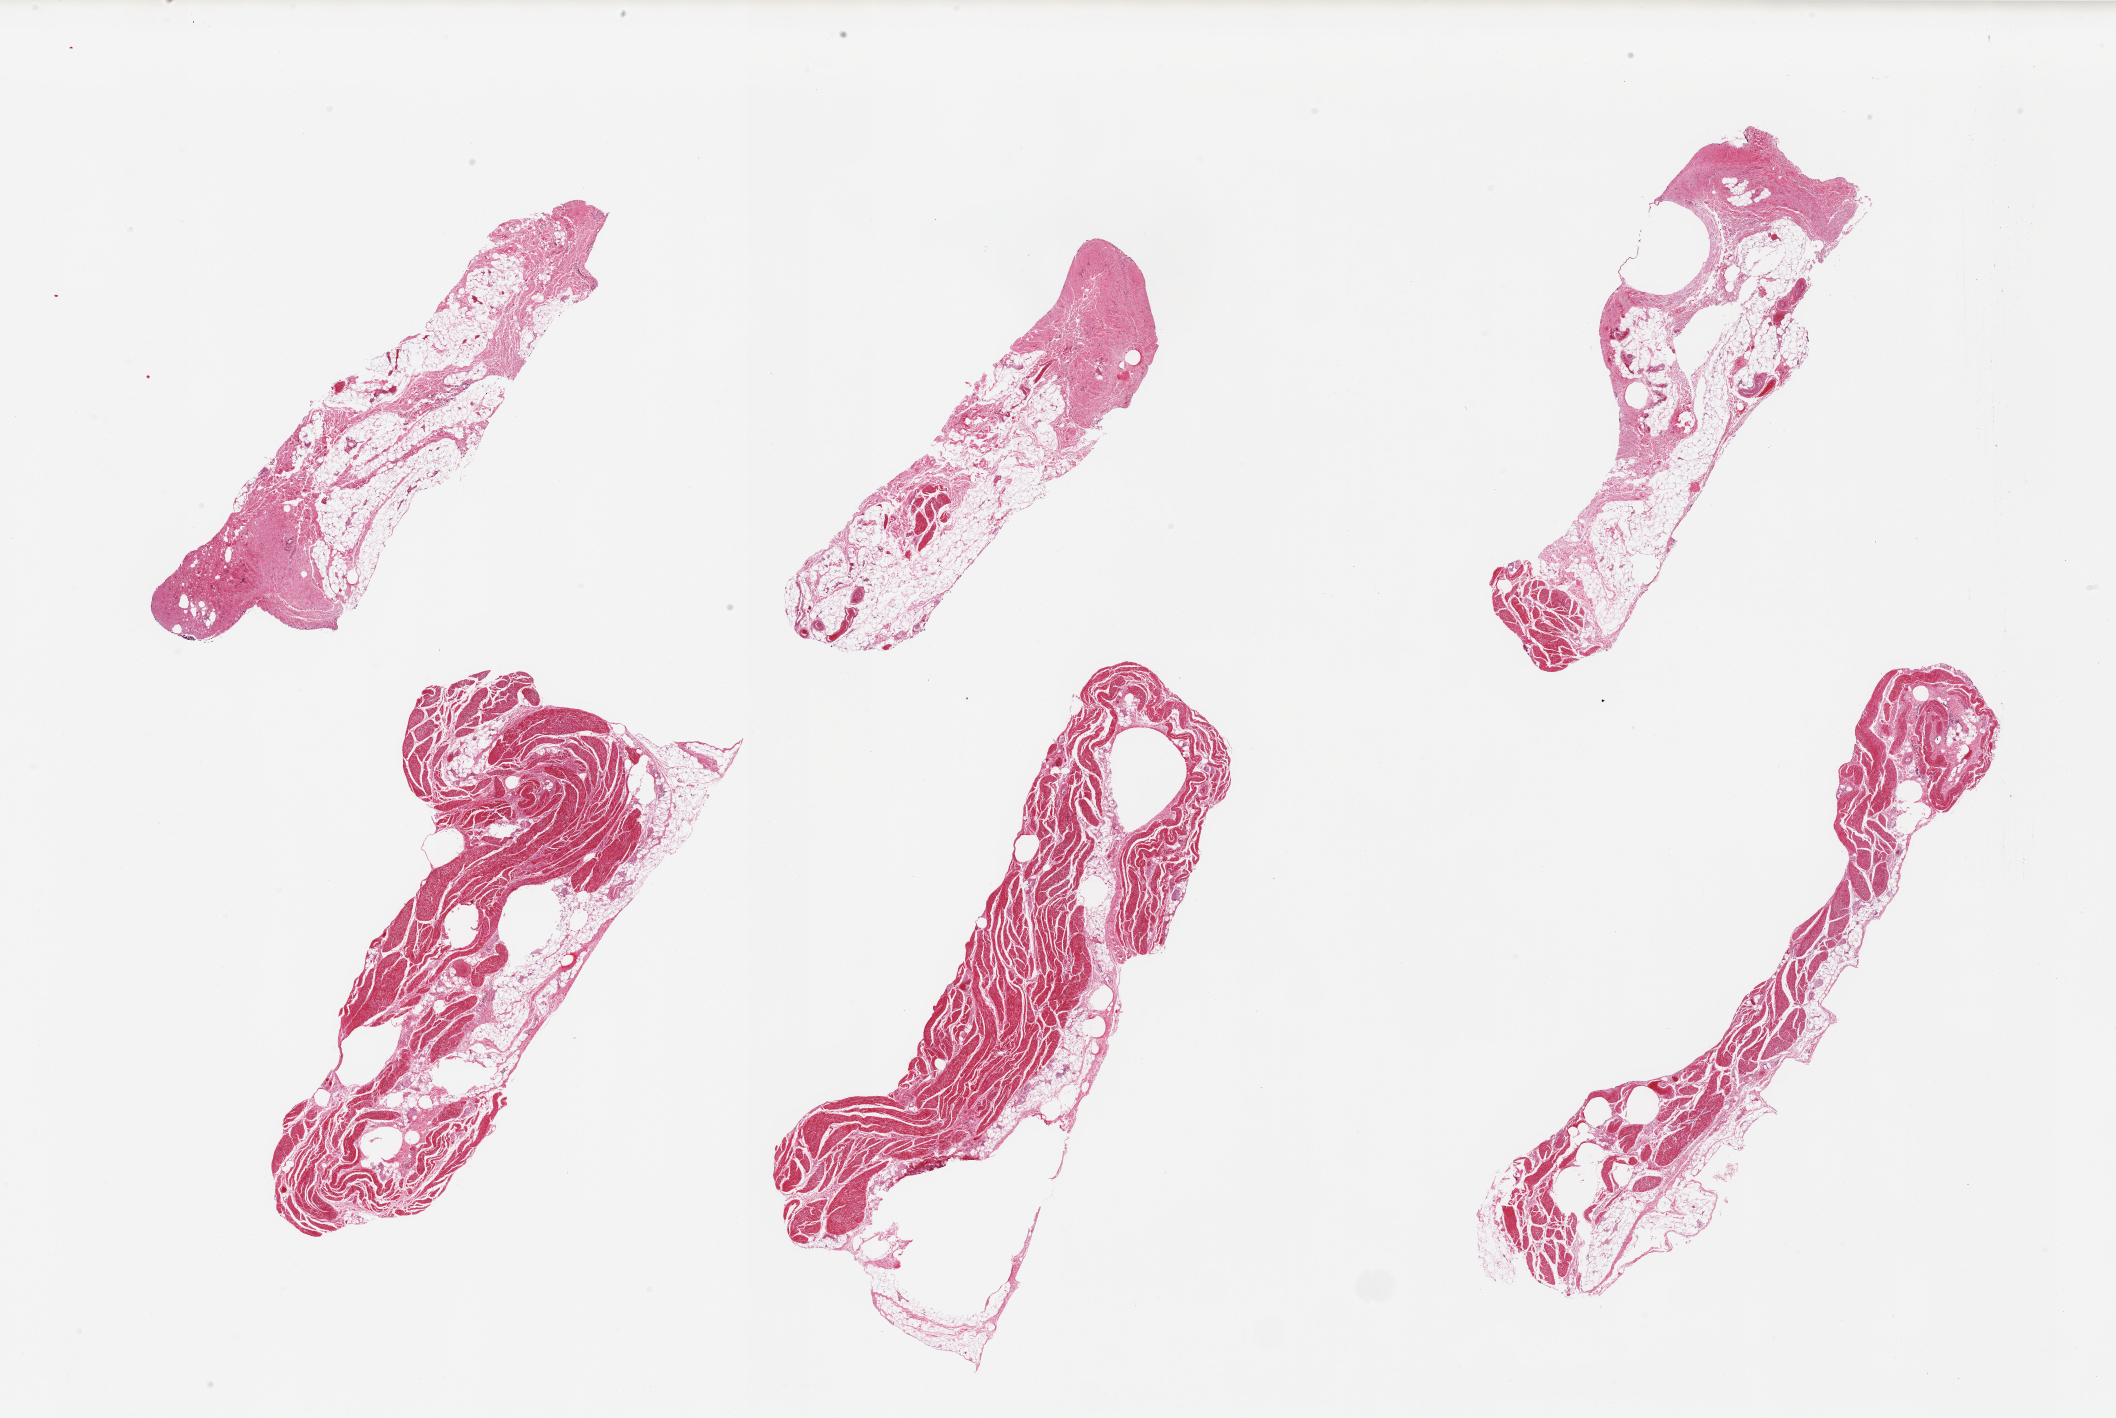
Haematoxylin and eosin whole-slide image, brightfield — shown as a low-resolution overview of the whole scanned area (about 33.5 x 22.4 mm); PAXgene-fixed, paraffin-embedded tissue; target tissue: vagina; donor tissue sample. Female donor.
• reviewer comment on this tissue sample: 6 pieces, fat and smooth muscle, unknown provenance. No squamous epithelium present